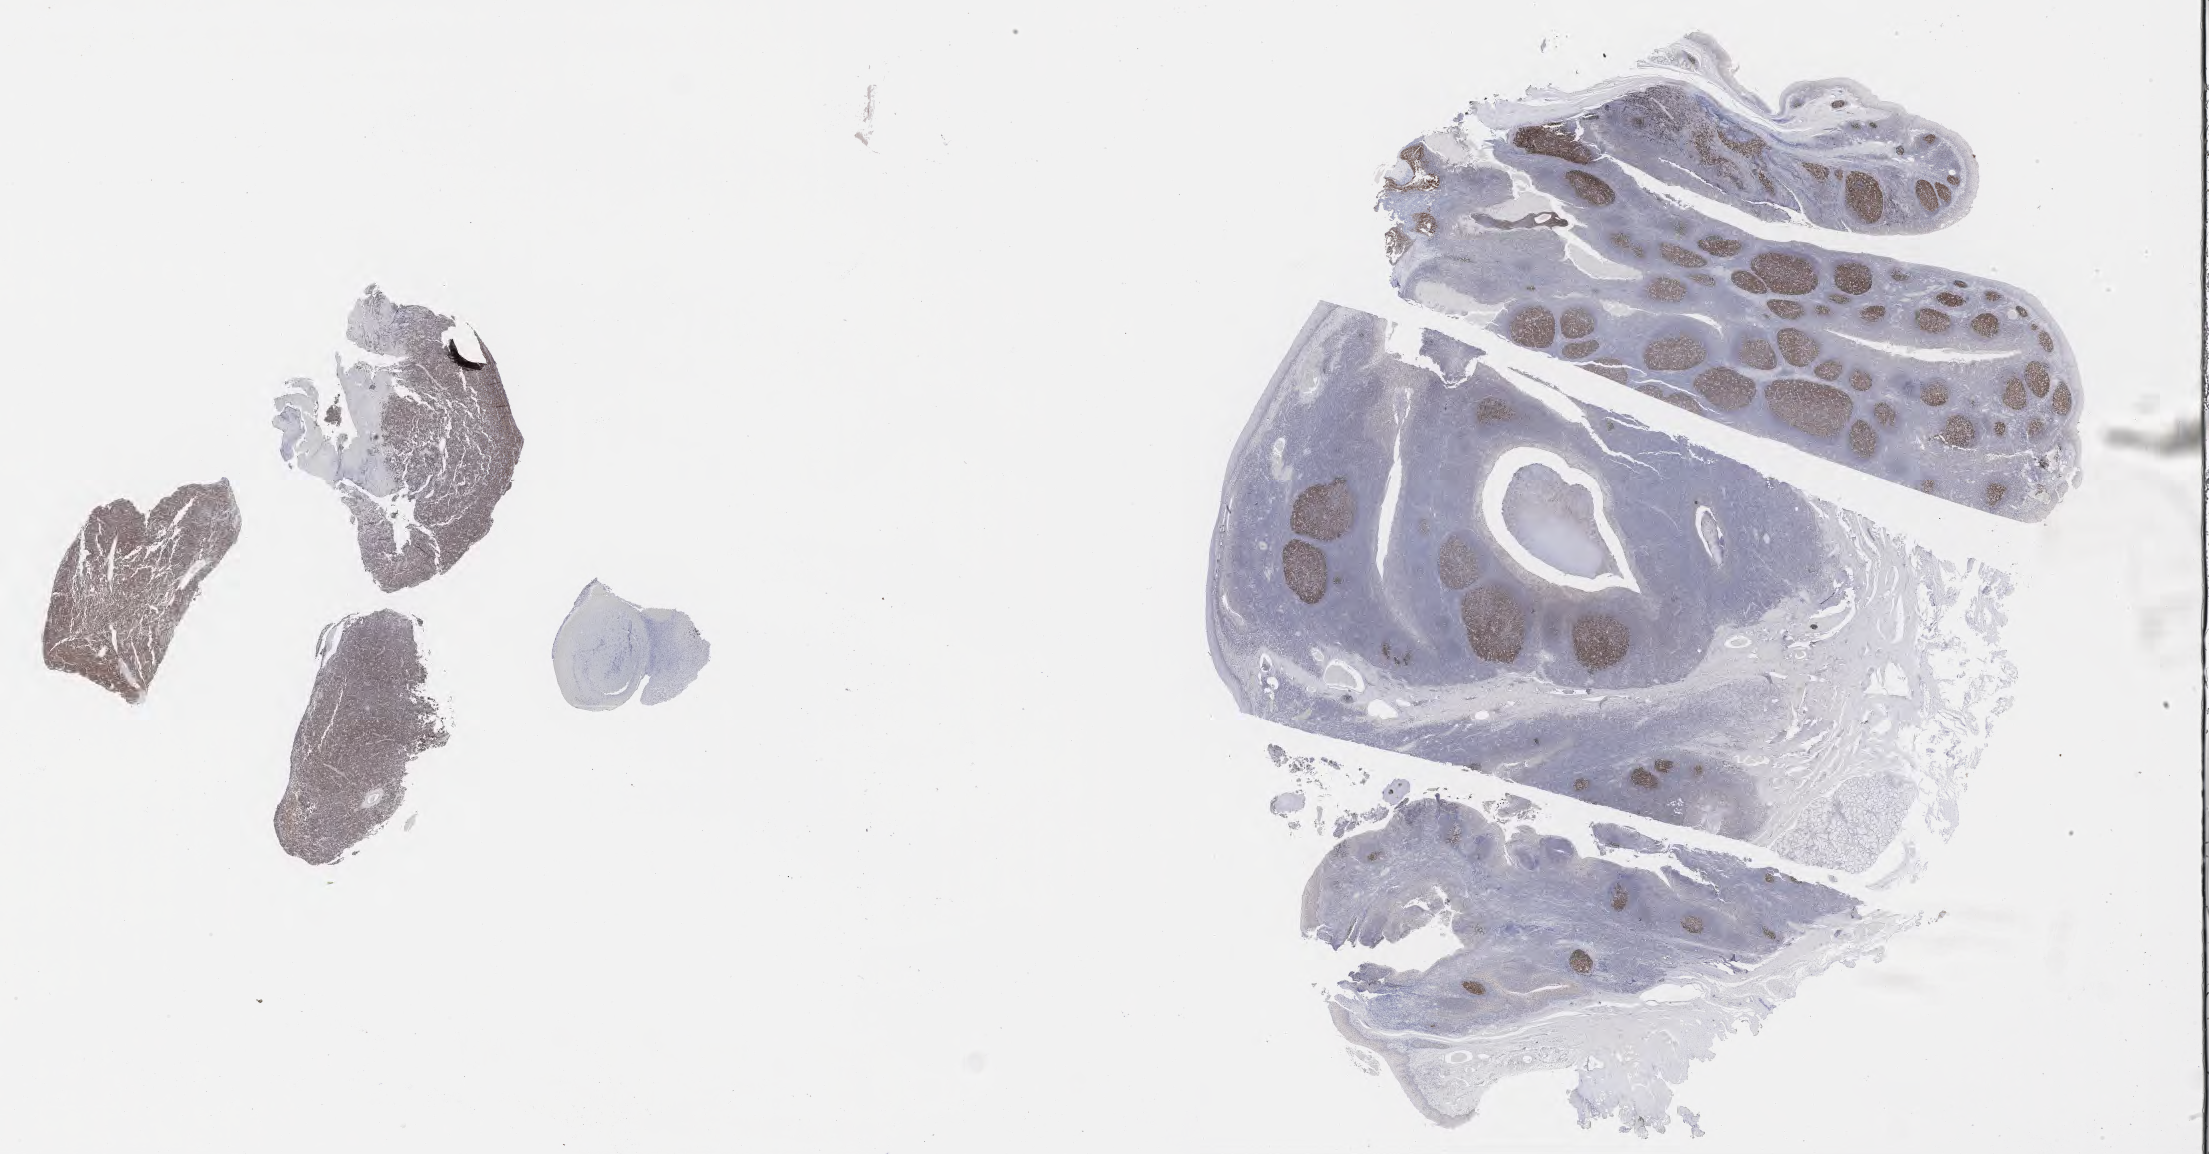
Immunohistochemistry (IHC) whole-slide image stained for BCL6, a low-resolution overview of the entire scanned area, about 35.7 x 18.7 mm; specimen: tumor tissue. Patient: male, aged 10.
Diagnosis: Burkitt lymphoma, NOS.